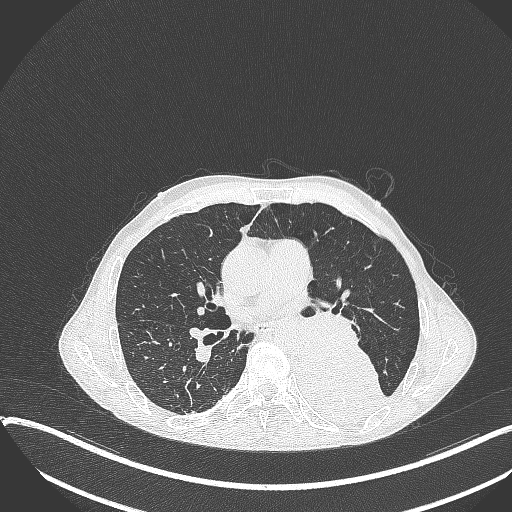
Chest CT, one axial slice. Slice 201 of 401 in the series (ordered by position). Reconstruction kernel B70f. 120 kVp. Lung window (W 1500 / L -600 HU). 1 mm slice thickness. 512 × 512 image matrix. Patient: male, 57 years. From the clinical record (not read from this slice): clinical TNM (as recorded): T4 N0 M0.
Outlined on this slice (bounding box drawn by a radiologist):
- lung tumour (recorded histology: squamous cell carcinoma): box from (x=291, y=345) to (x=388, y=422) px